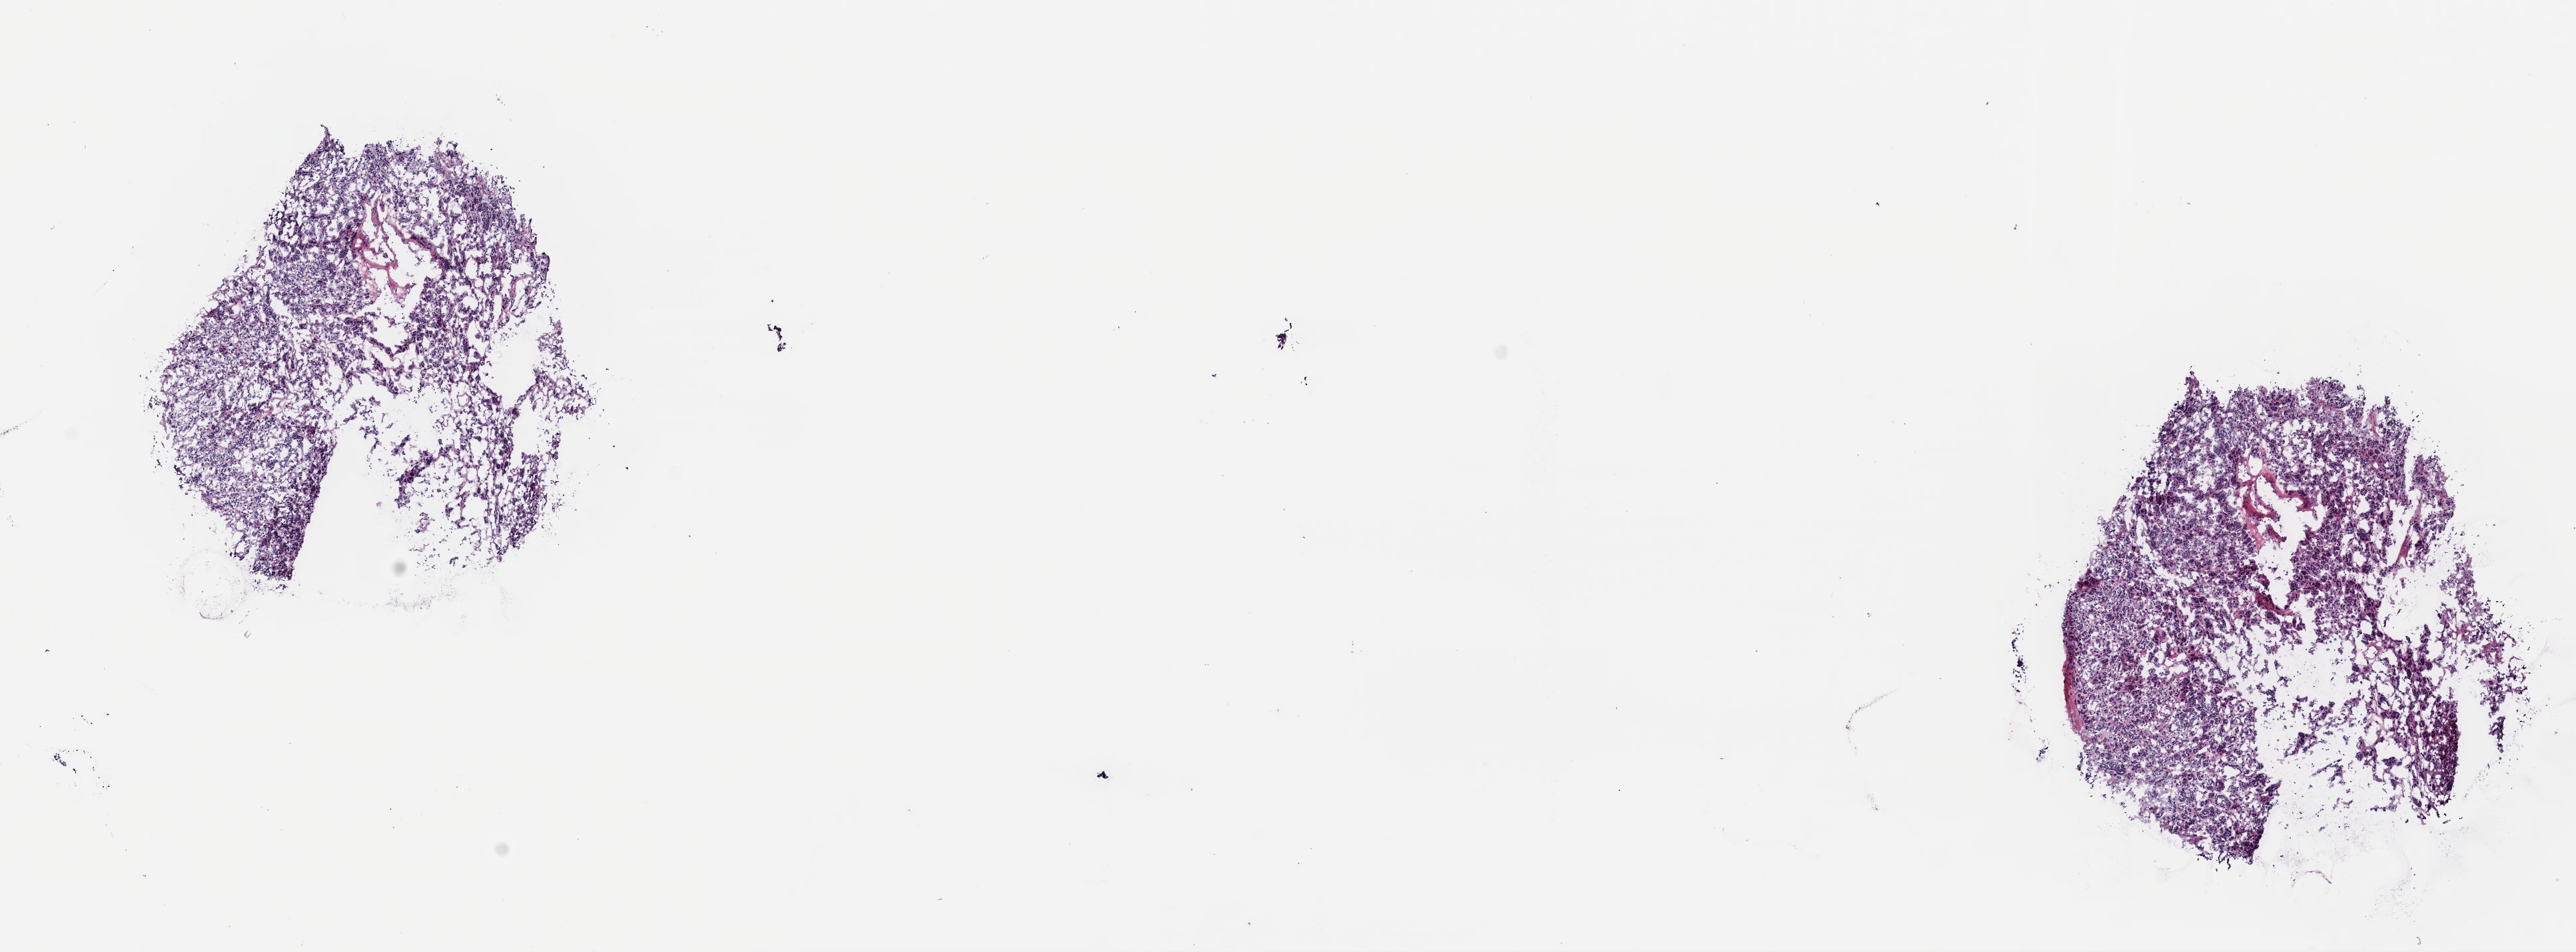
Whole-slide histology image, Hematoxylin and eosin (H&E) stained — a low-resolution overview of the entire scanned area, about 15.3 x 5.6 mm. Frozen section from the top of the tissue portion. Sample: primary tumour, thyroid. Female patient; age at initial diagnosis 42 years. Pathologist review of this section (percent, as recorded): tumour cells 80%, tumour nuclei 80%, normal cells 3%, stromal cells 17%, necrosis 0%. Inflammatory infiltration, as recorded: lymphocyte infiltration 1%, monocyte infiltration 0%, neutrophil infiltration 0%.
• AJCC pathologic stage: I (7th edition)
• pathologic diagnosis: Papillary carcinoma, follicular variant (thyroid gland)
• laterality: left